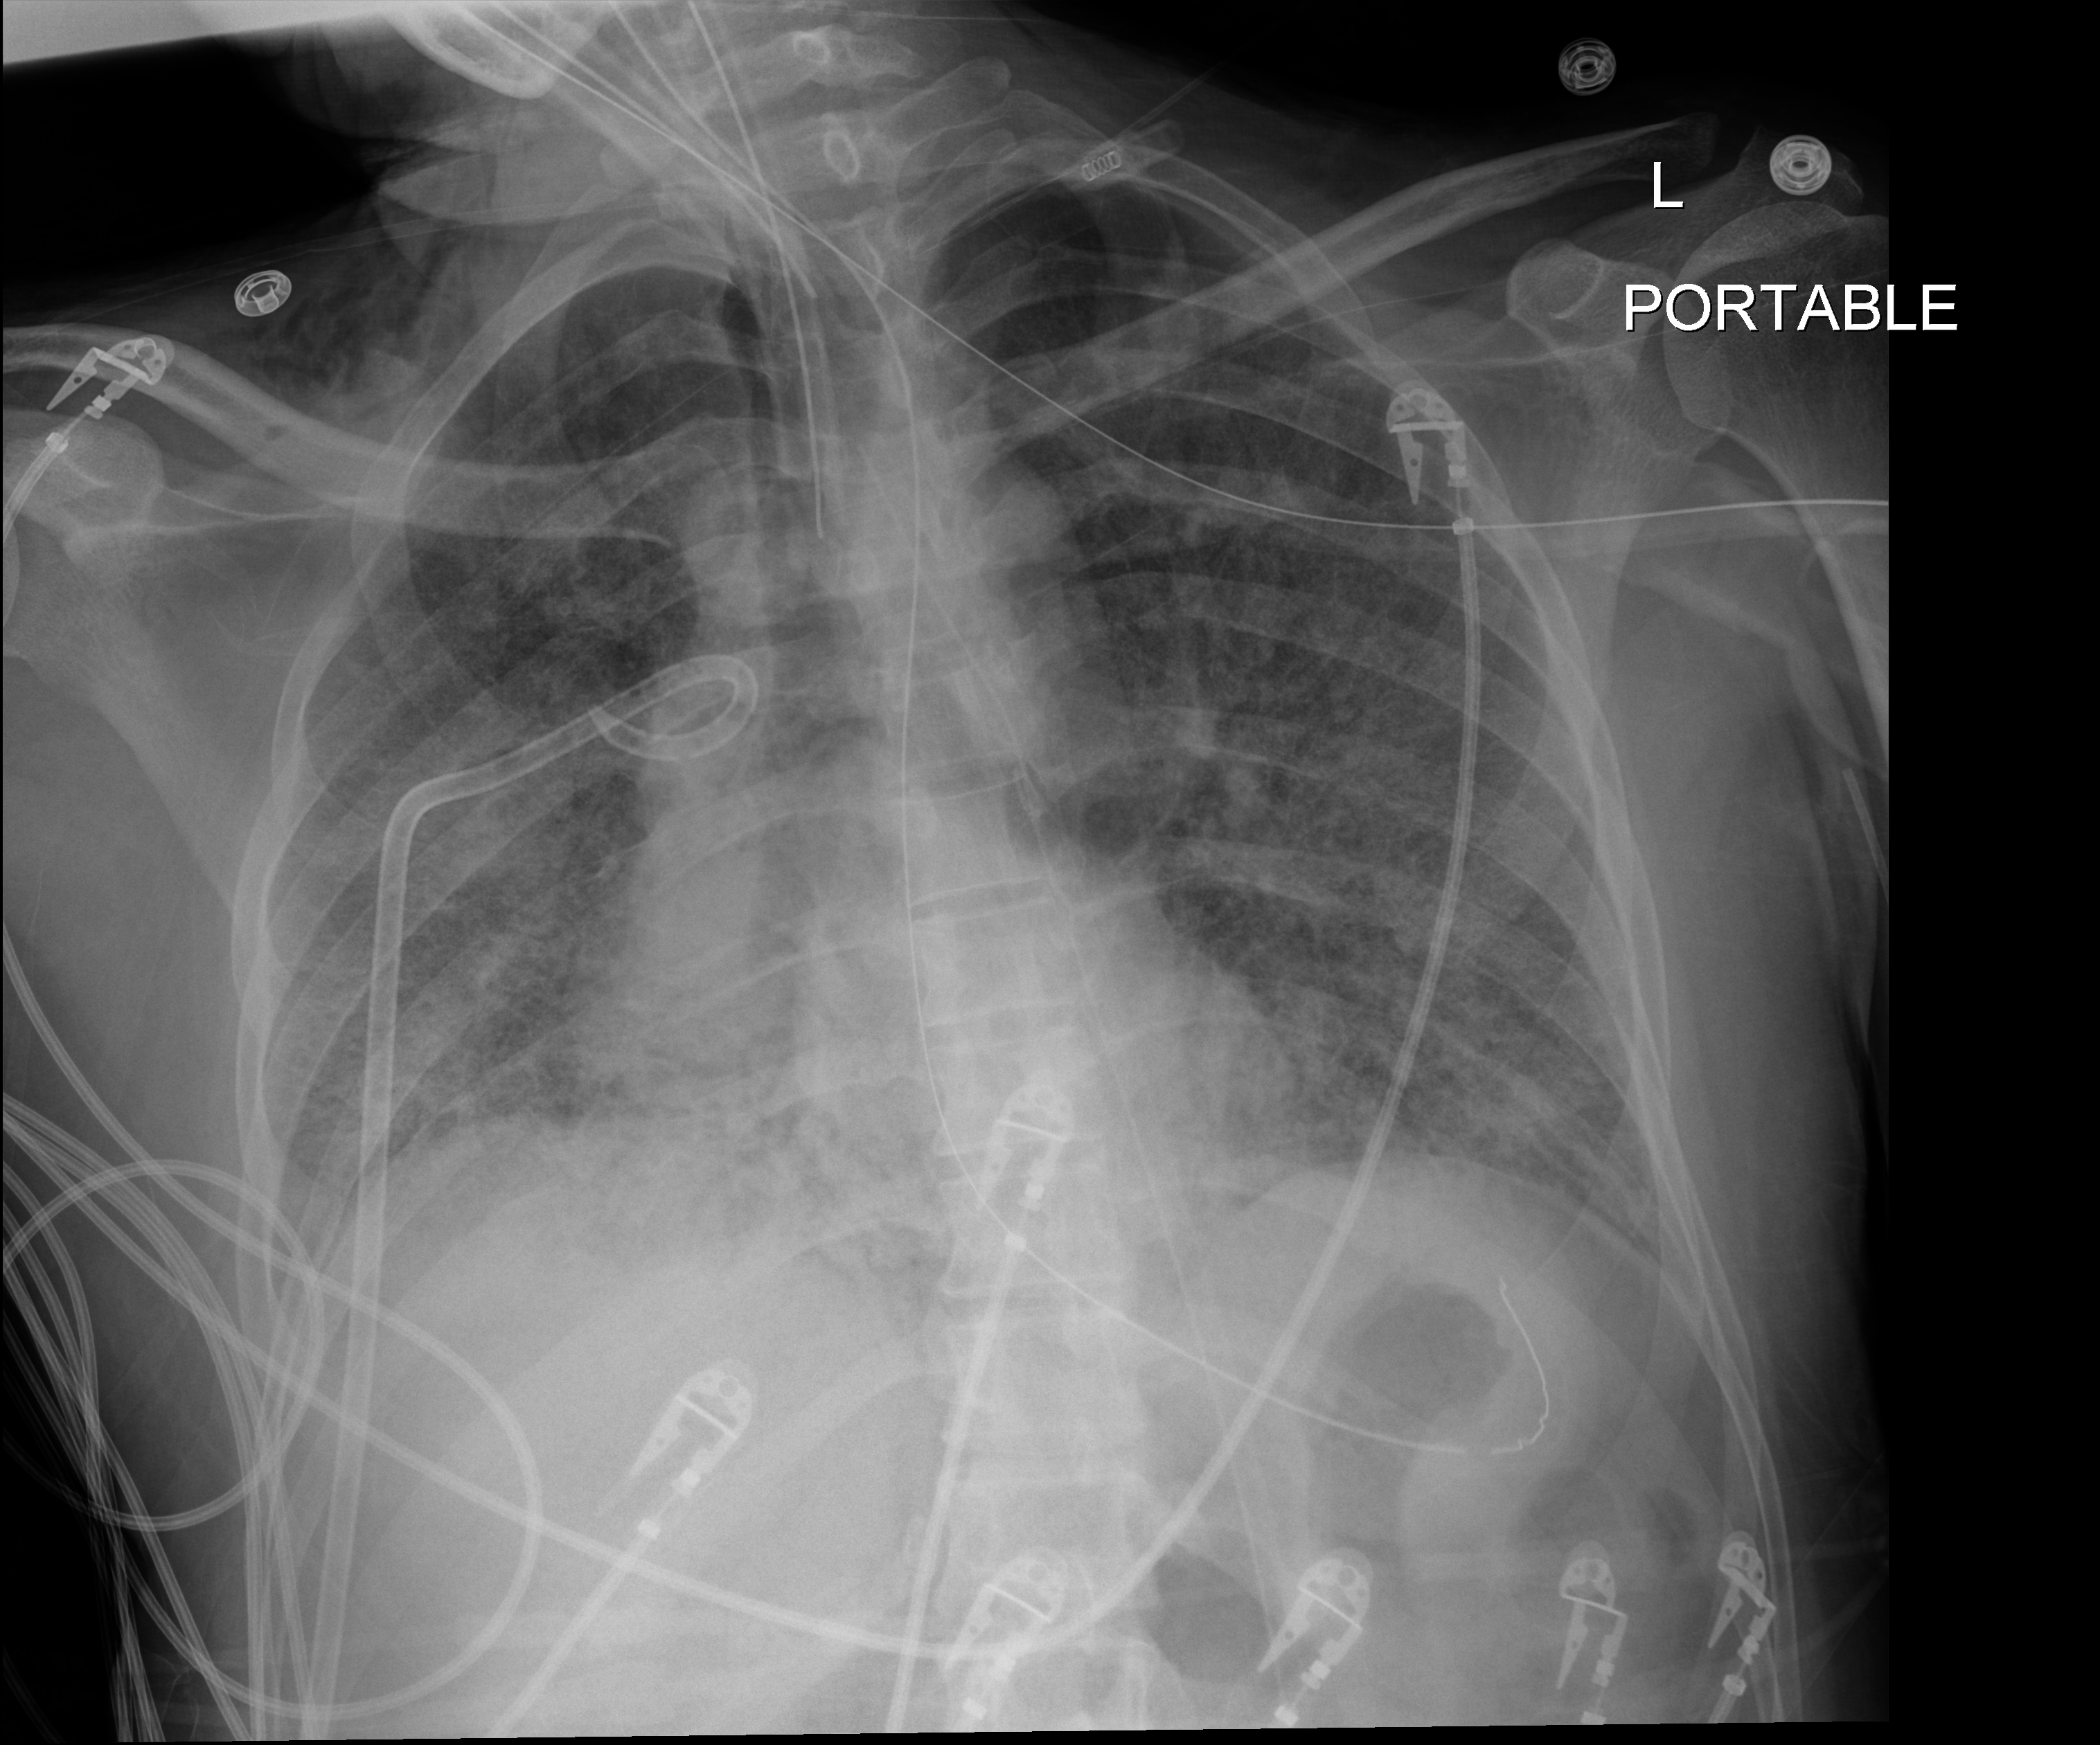
Bedside chest radiograph (digital radiography), anteroposterior (AP) projection. Adult patient hospitalised with COVID-19, age 18–59 years.
Admission-level facts for this patient (not findings on this image; timing relative to this image not recorded): mechanically ventilated during this hospital stay: yes; smoking status (admission record): never; length of hospital stay: 41 days.